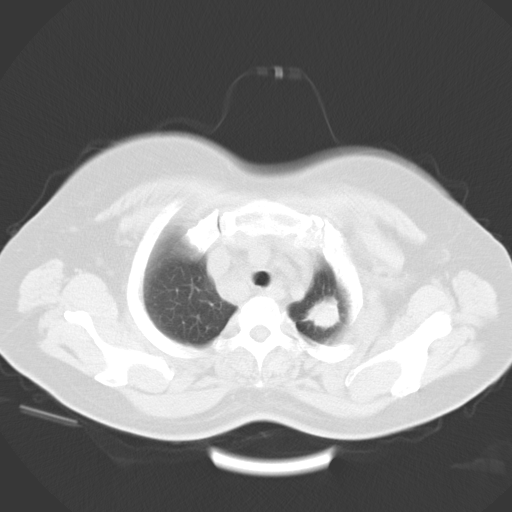
Chest CT, one axial slice; position 26 of 29 along the scan axis; lung window (W 1500 / L -600 HU); 10 mm slice thickness; 512 × 512 image matrix, field of view 390 × 390 mm. Female patient, age 53 years. From the clinical record (not read from this slice): clinical TNM (as recorded): T1c N3 M0.
Annotated regions visible in this slice (rectangle marked by the reading radiologist):
- lung tumour (recorded histology: adenocarcinoma): bounding box [x1, y1, x2, y2] px = [304, 295, 339, 334]